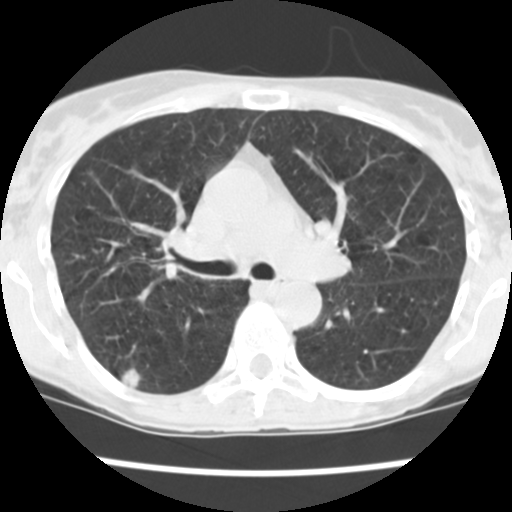
Low-dose screening chest CT, one axial slice. Position 153 of 252 along the scan axis. Reconstruction kernel STANDARD. 120 kVp. Lung window (W 1500 / L -600 HU). 2.5 mm slice thickness. 512 × 512 image matrix, field of view 276 × 276 mm.
Structures marked on this image (expert manual segmentation):
- lesion 1 (tumor, upper lobe of right lung): bounding box [x1, y1, x2, y2] px = [122, 368, 141, 390]